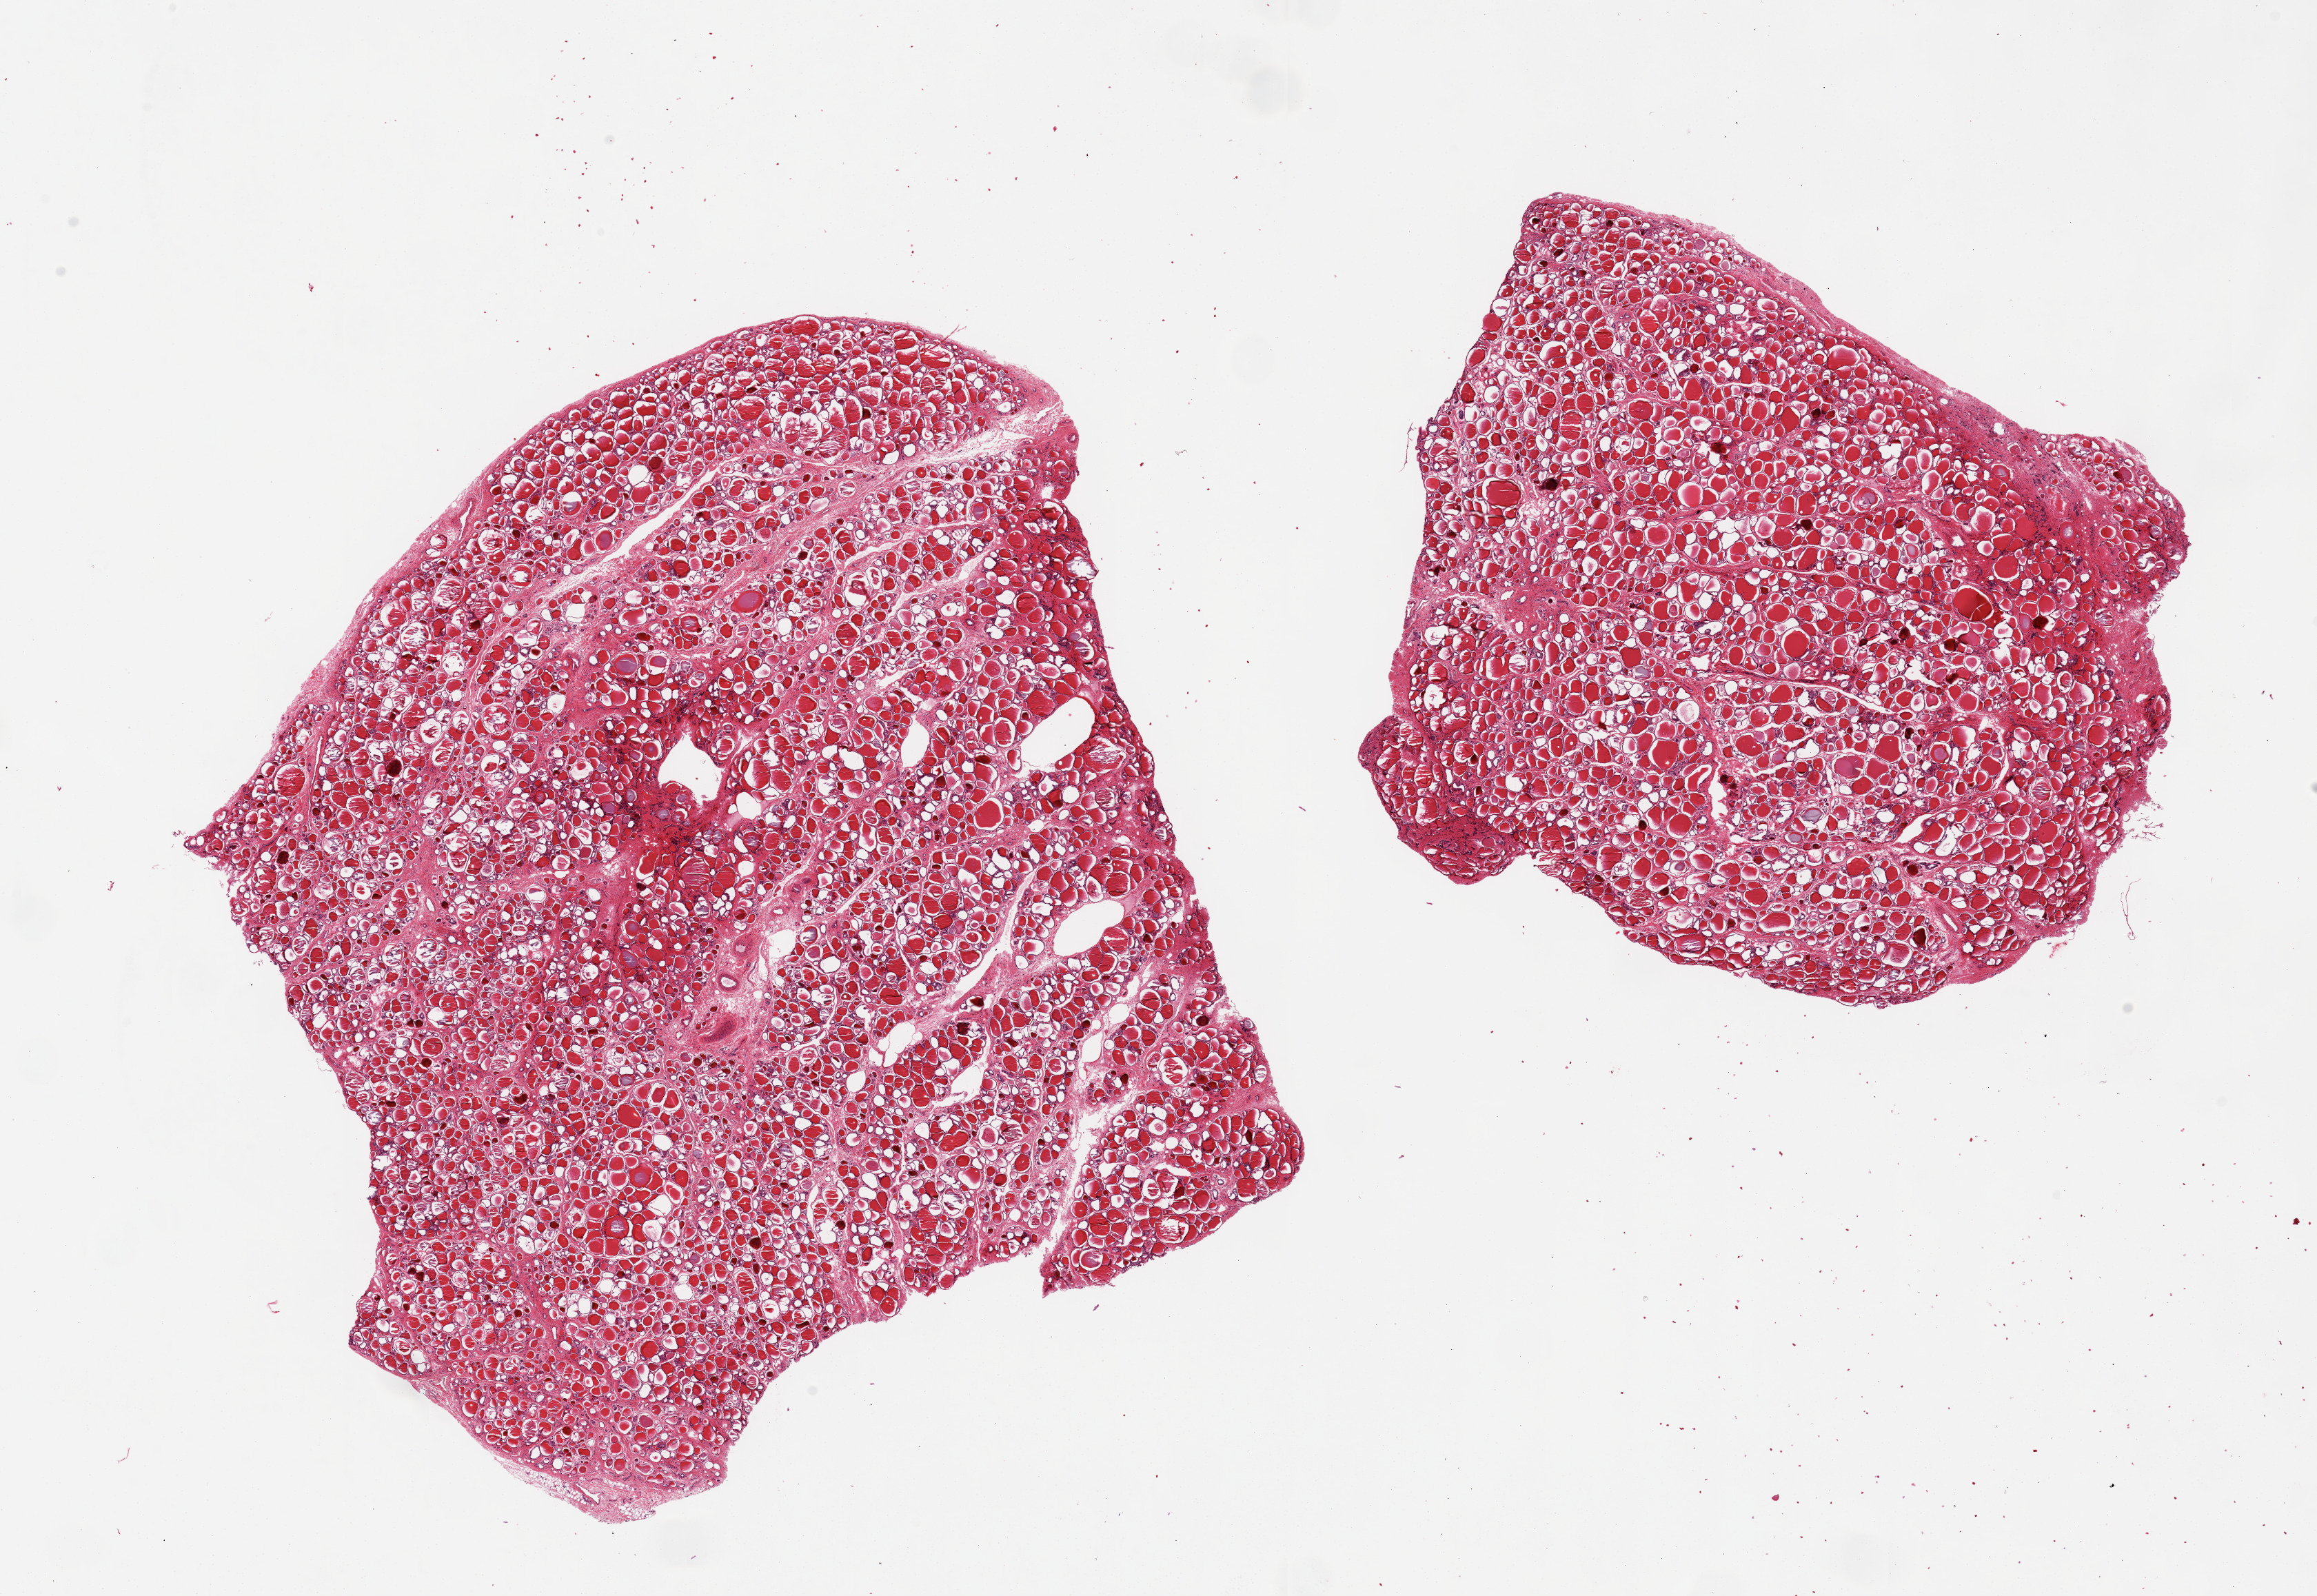
H&E whole-slide image, brightfield, low-resolution overview of the scanned area, about 26.6 x 18.3 mm (acquisition: 20x scan). PAXgene-fixed paraffin-embedded (PFPE) section. Target tissue: thyroid. Donor tissue sample. Donor sex: female.
• review note (as recorded): 2 pieces, no abnormalities